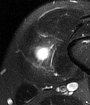
MRI of an extremity soft-tissue mass, one axial slice; position 13 of 65 along the scan axis; T2-weighted fat-saturated; MR volume resampled by the dataset authors to the PET/CT grid (not the native acquisition matrix); 90 × 105 image matrix, field of view 88 × 103 mm. Male patient. Case-level facts recorded for this patient, not image findings: histological type: mixoid liposarcoma; grade: low; site of the primary tumour: left thigh.
Structures marked on this image (expert contour drawn on MRI and transferred to this co-registered scan by the dataset authors):
- gross tumour volume (mass): box from (x=34, y=44) to (x=51, y=60) px